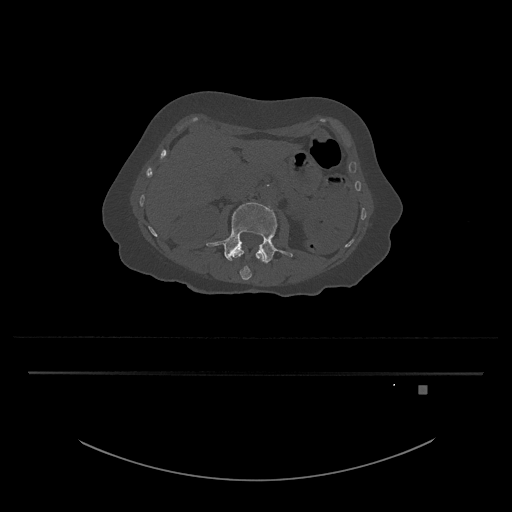
CT including the spine, one axial slice; slice 449 of 797 in the series (ordered by position); 120 kVp; bone window (W 1800 / L 400 HU); 0.5 mm slice thickness; 512 × 512 image matrix, field of view 500 × 500 mm. Female patient, age 57 years. Case-level facts recorded for this patient, not image findings: primary cancer: cervical.
Structures marked on this image (semi-automatic segmentation, software-assisted and operator-edited):
- L3 vertebra: bounding box (x1, y1, x2, y2) in pixels: (206, 202, 293, 264)